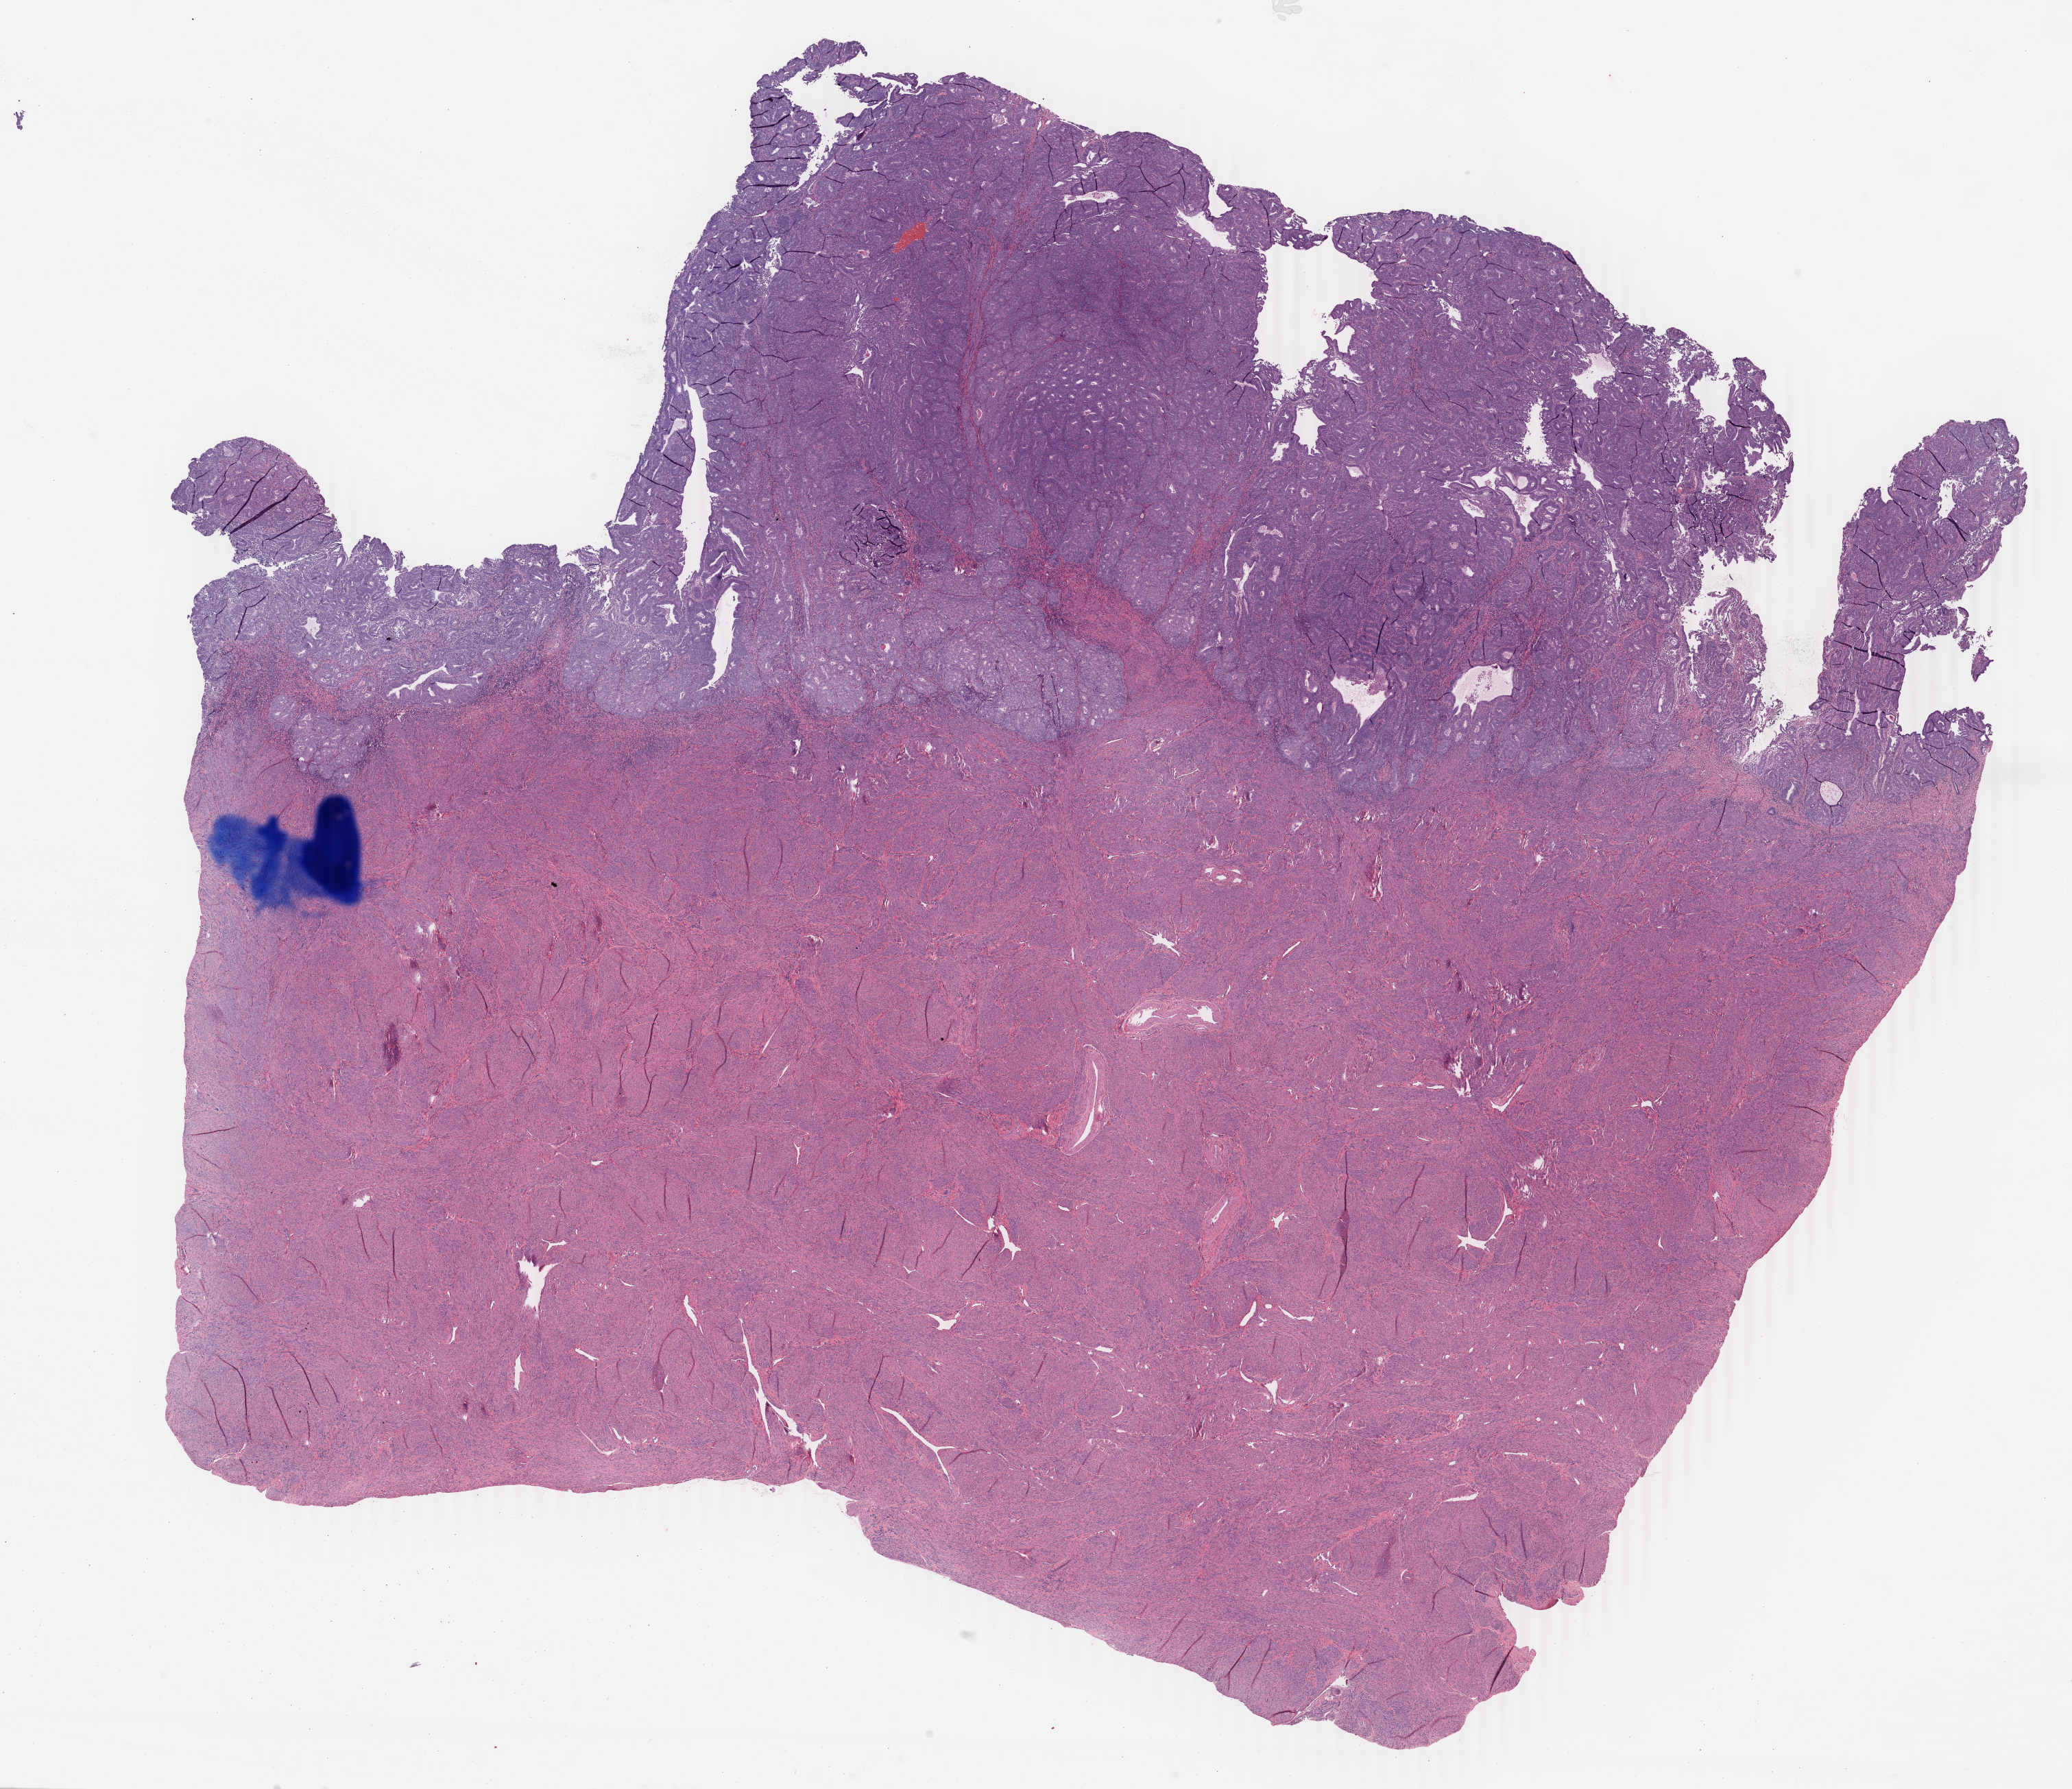
Whole-slide histology image, H&E, a low-resolution overview of the entire scanned area, about 24.0 x 20.7 mm (acquisition: 40x scan). Formalin-fixed paraffin-embedded (FFPE) diagnostic section. Uterus, primary tumour sample. Female, age 57 years at initial diagnosis. Histologic grade: G1 (well differentiated).
FIGO stage: IA. Diagnosis: Endometrioid adenocarcinoma, NOS (endometrium).